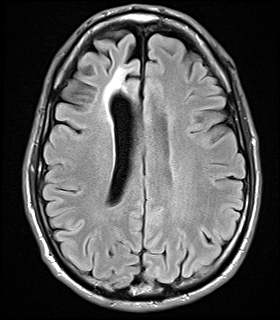
Brain MRI from a brain-tumour surgery series, one axial slice; position 12 of 32 along the scan axis; T2 FLAIR; 280 × 320 image matrix, field of view 184 × 210 mm. From the clinical record (not read from this slice): histopathology: Glial fibroma; tumour location: Right Frontal.
Structures marked on this image (outlined manually by an expert reader):
- tumour: box from (x=105, y=64) to (x=140, y=121) px